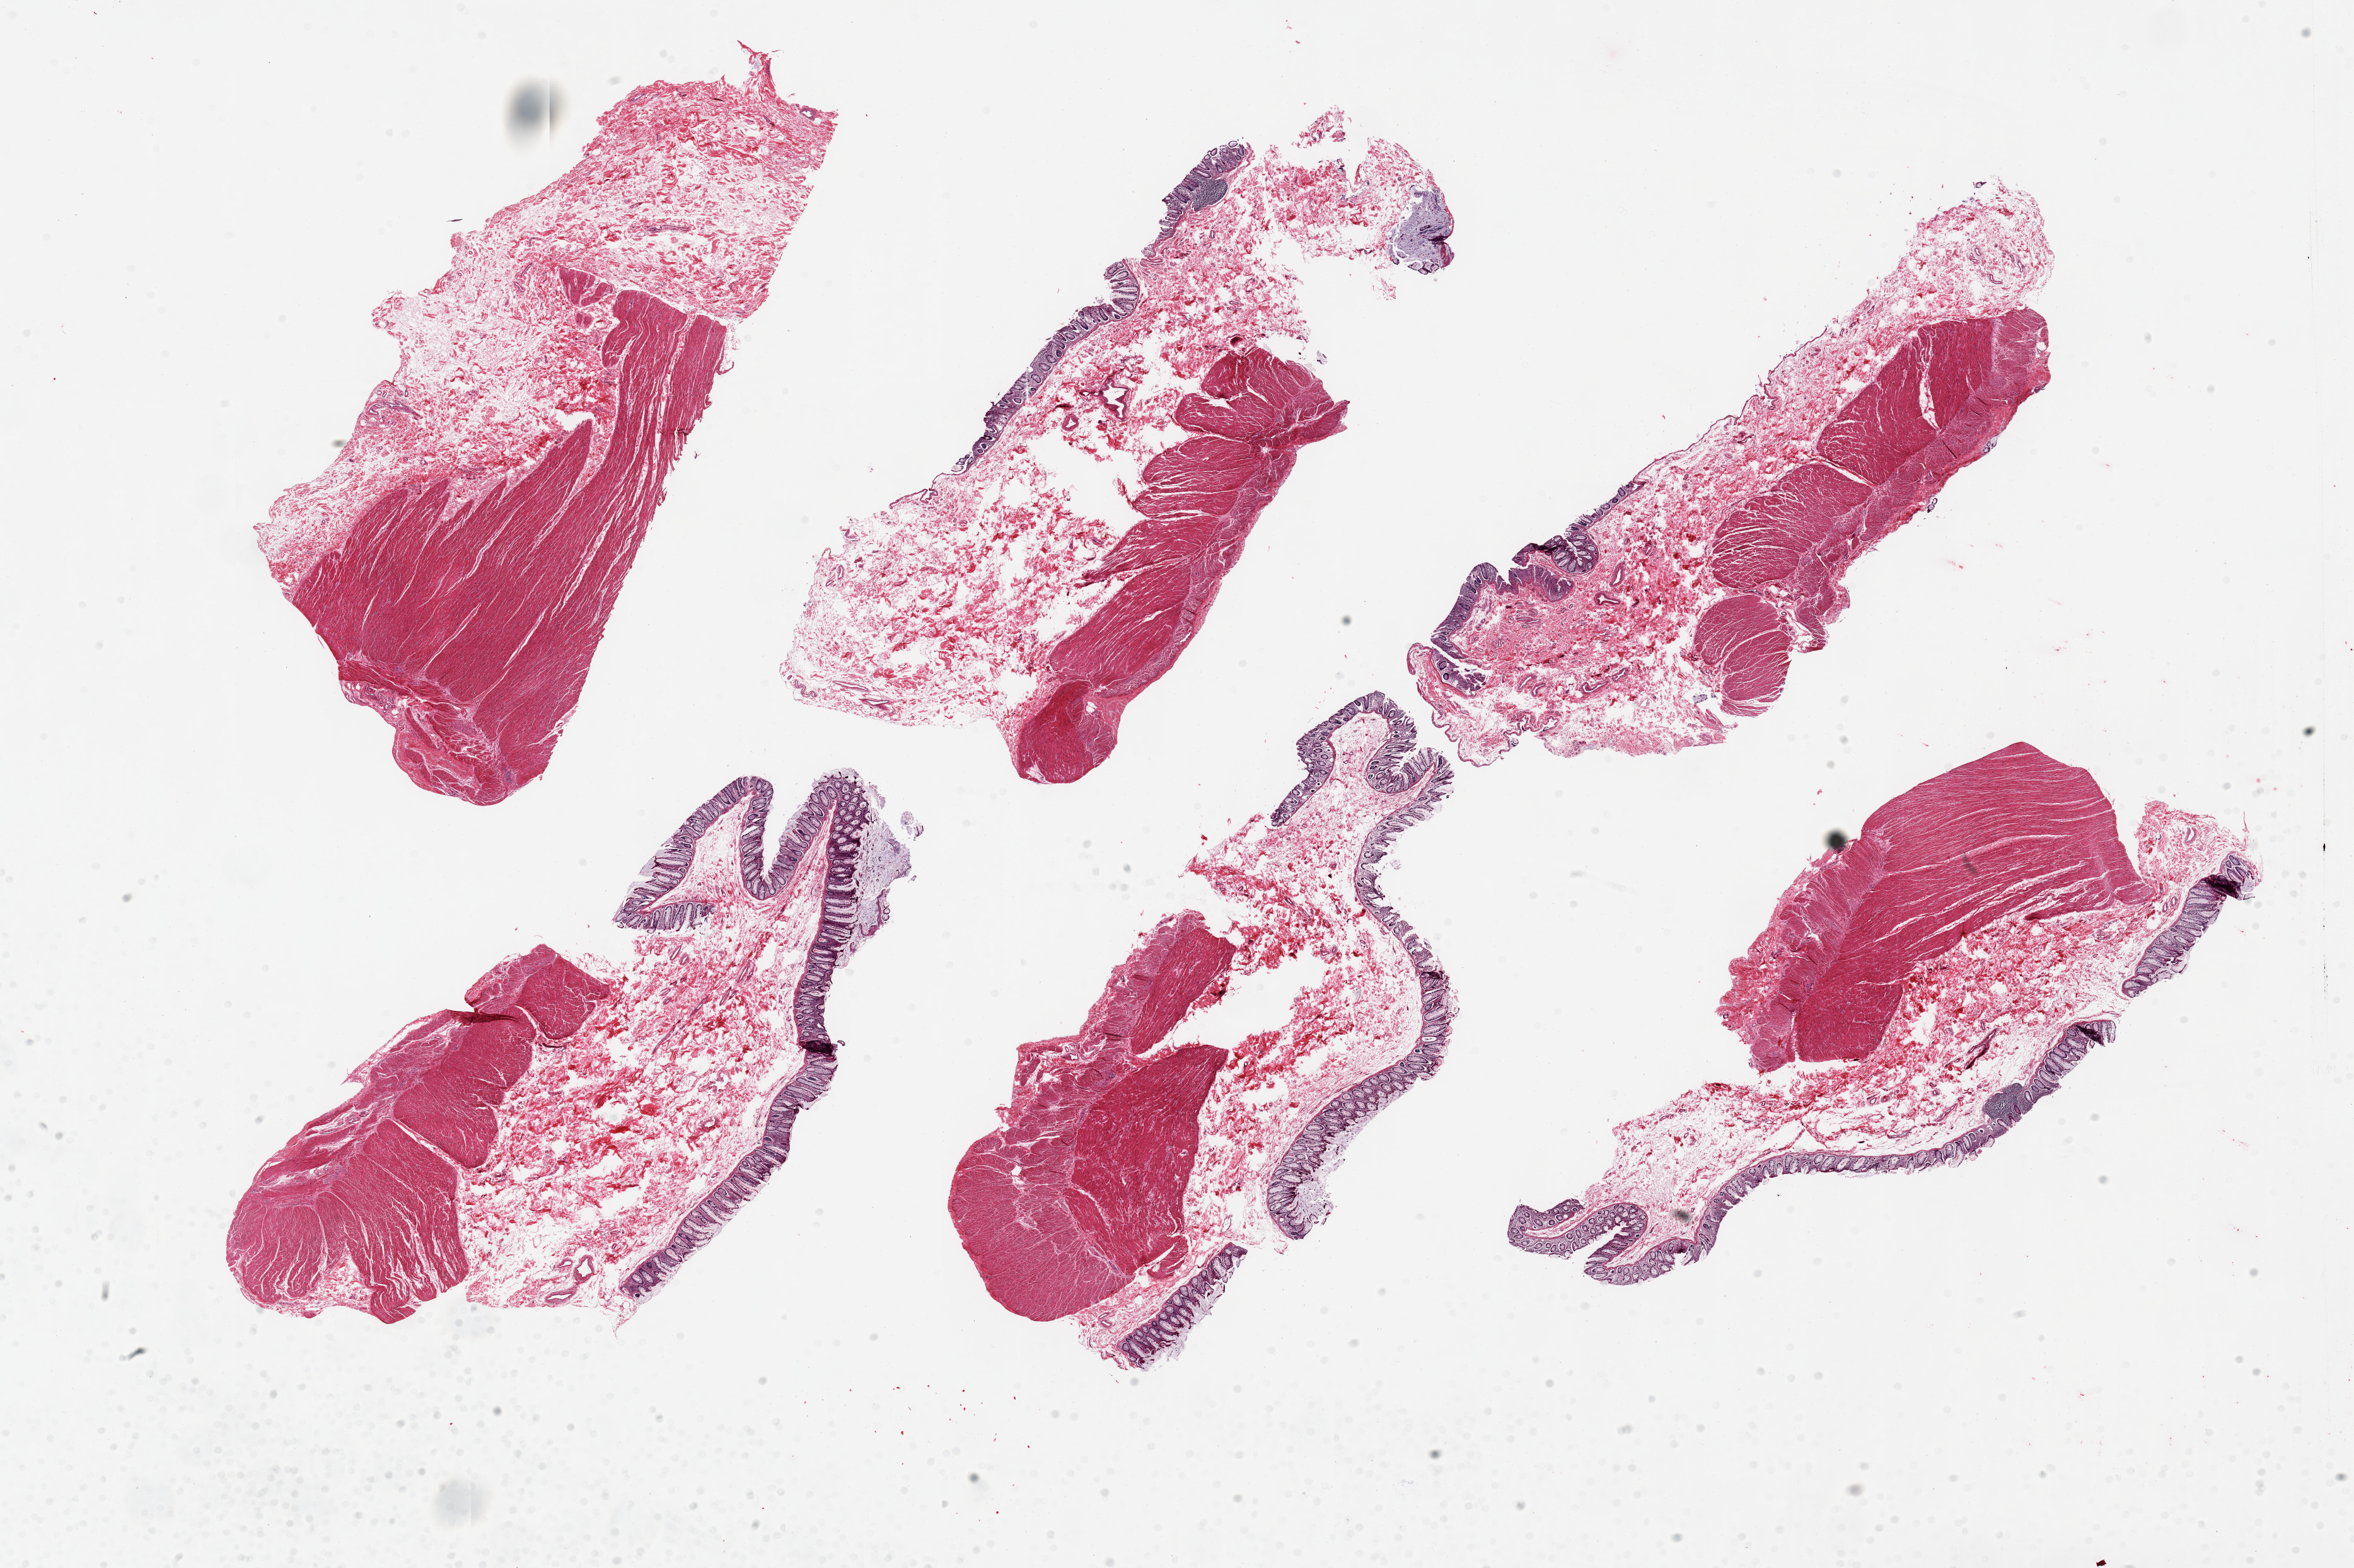
Digitized H&E-stained section, brightfield, low-resolution overview of the scanned area, about 29.5 x 19.7 mm (acquisition: 20x scan). PAXgene-fixed paraffin-embedded (PFPE) section. Target tissue: transverse colon. Tissue donor sample.
Pathologist's review note for this sample: 6 pieces; 1 is without mucosa.